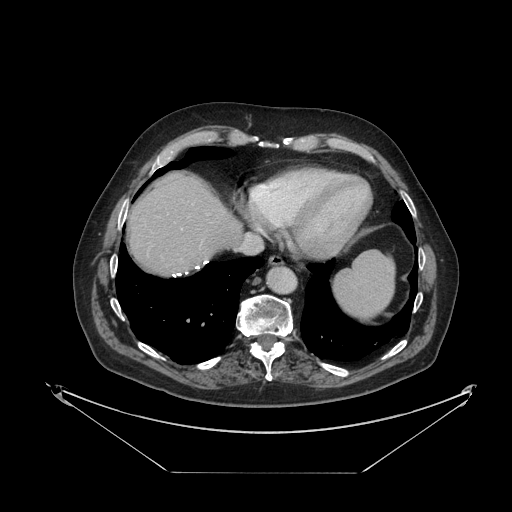
Contrast-enhanced abdominal CT, one axial slice. Slice 108 of 121 in the series (ordered by position). Reconstruction kernel STANDARD. Intravenous contrast given. Soft-tissue window (W 400 / L 40 HU). 2.5 mm slice thickness. 512 × 512 image matrix. Male patient, age 68 years. Case-level facts recorded for this patient, not image findings: diagnosis: colorectal cancer liver metastases, imaged before liver resection; multiple liver metastases: no.
Annotated regions visible in this slice (expert manual segmentation):
- liver: bounding box [x1, y1, x2, y2] px = [130, 175, 241, 275]
- planned liver remnant (the part of the liver to remain after resection): [130, 175, 241, 275]